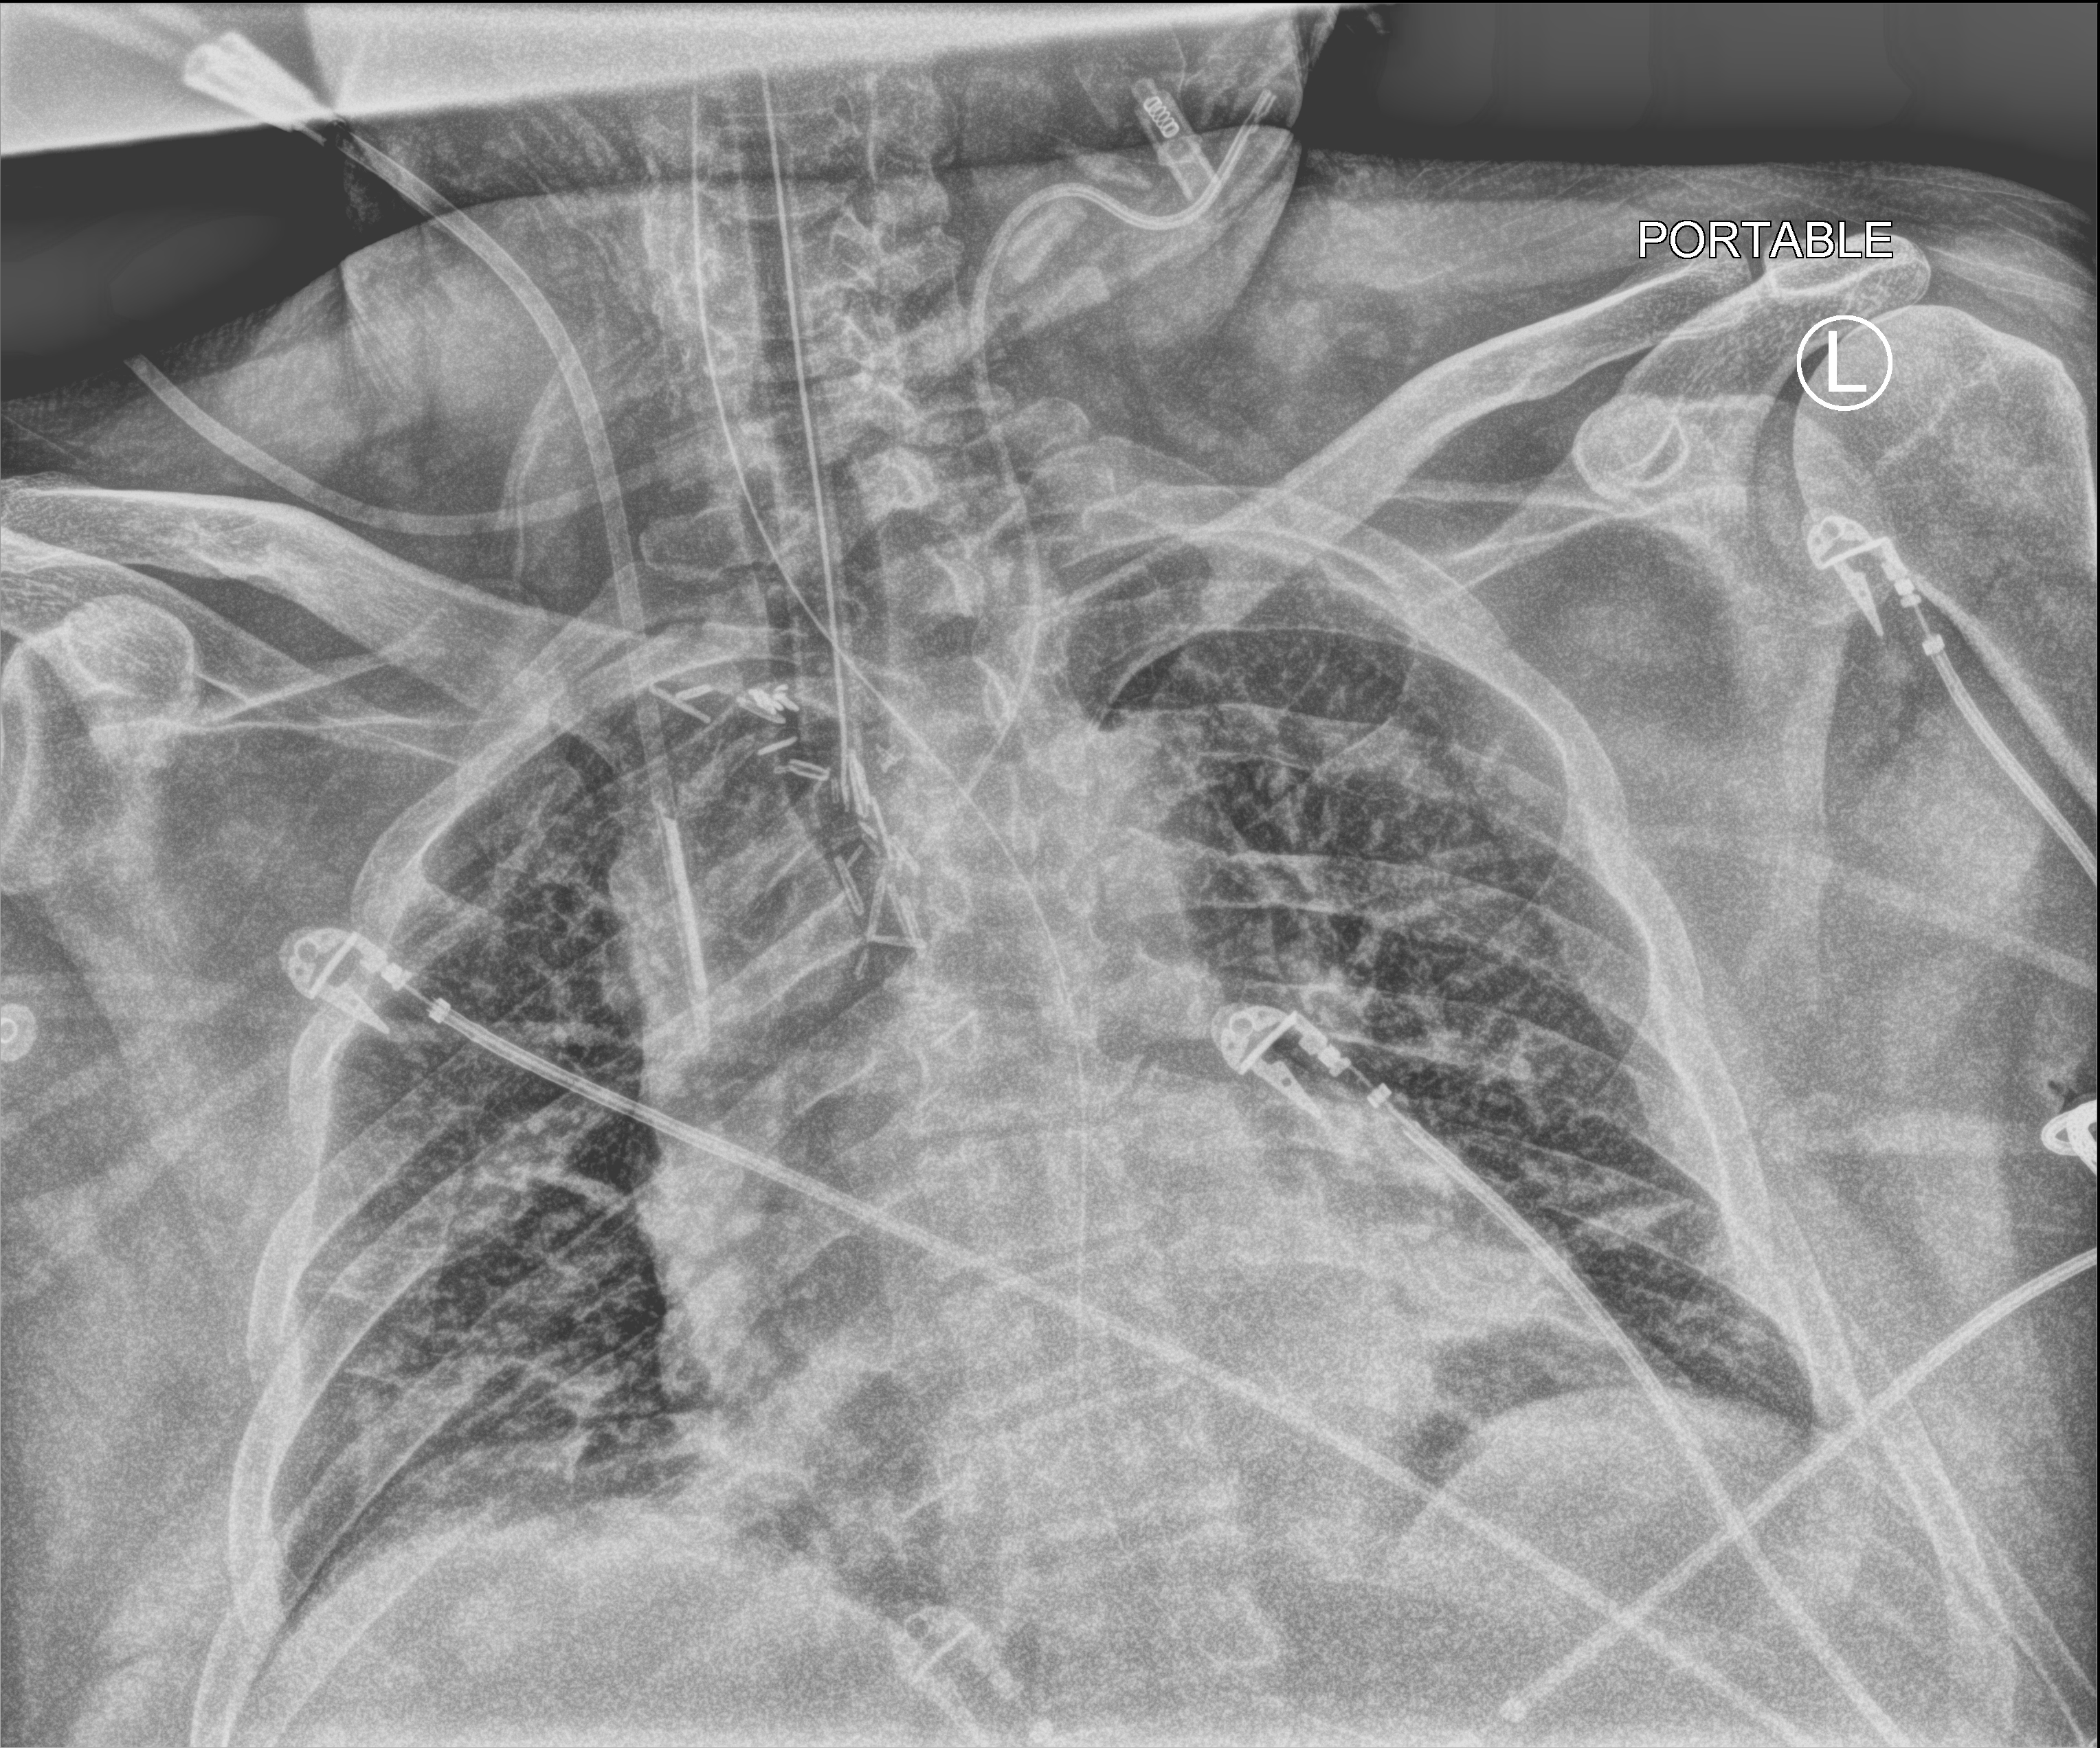
Chest X-ray (portable). Adult patient hospitalised with COVID-19, age 18–59 years.
From the hospital-stay record, not from the radiograph (when in the stay this image was taken is not recorded): mechanically ventilated during this hospital stay: yes.